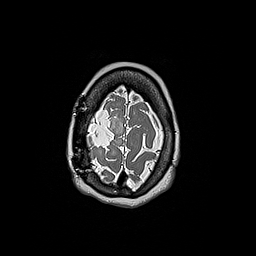
Brain MRI from a brain-tumour surgery series, one axial slice. Slice 43 of 192 in the series (ordered by position). 1 mm slice thickness. 256 × 256 image matrix. From the clinical record (not read from this slice): histopathology: Oligodendroglioma; WHO grade: 3; IDH mutation: yes.
Annotated regions visible in this slice (expert manual segmentation):
- tumour: box from (x=87, y=137) to (x=96, y=149) px